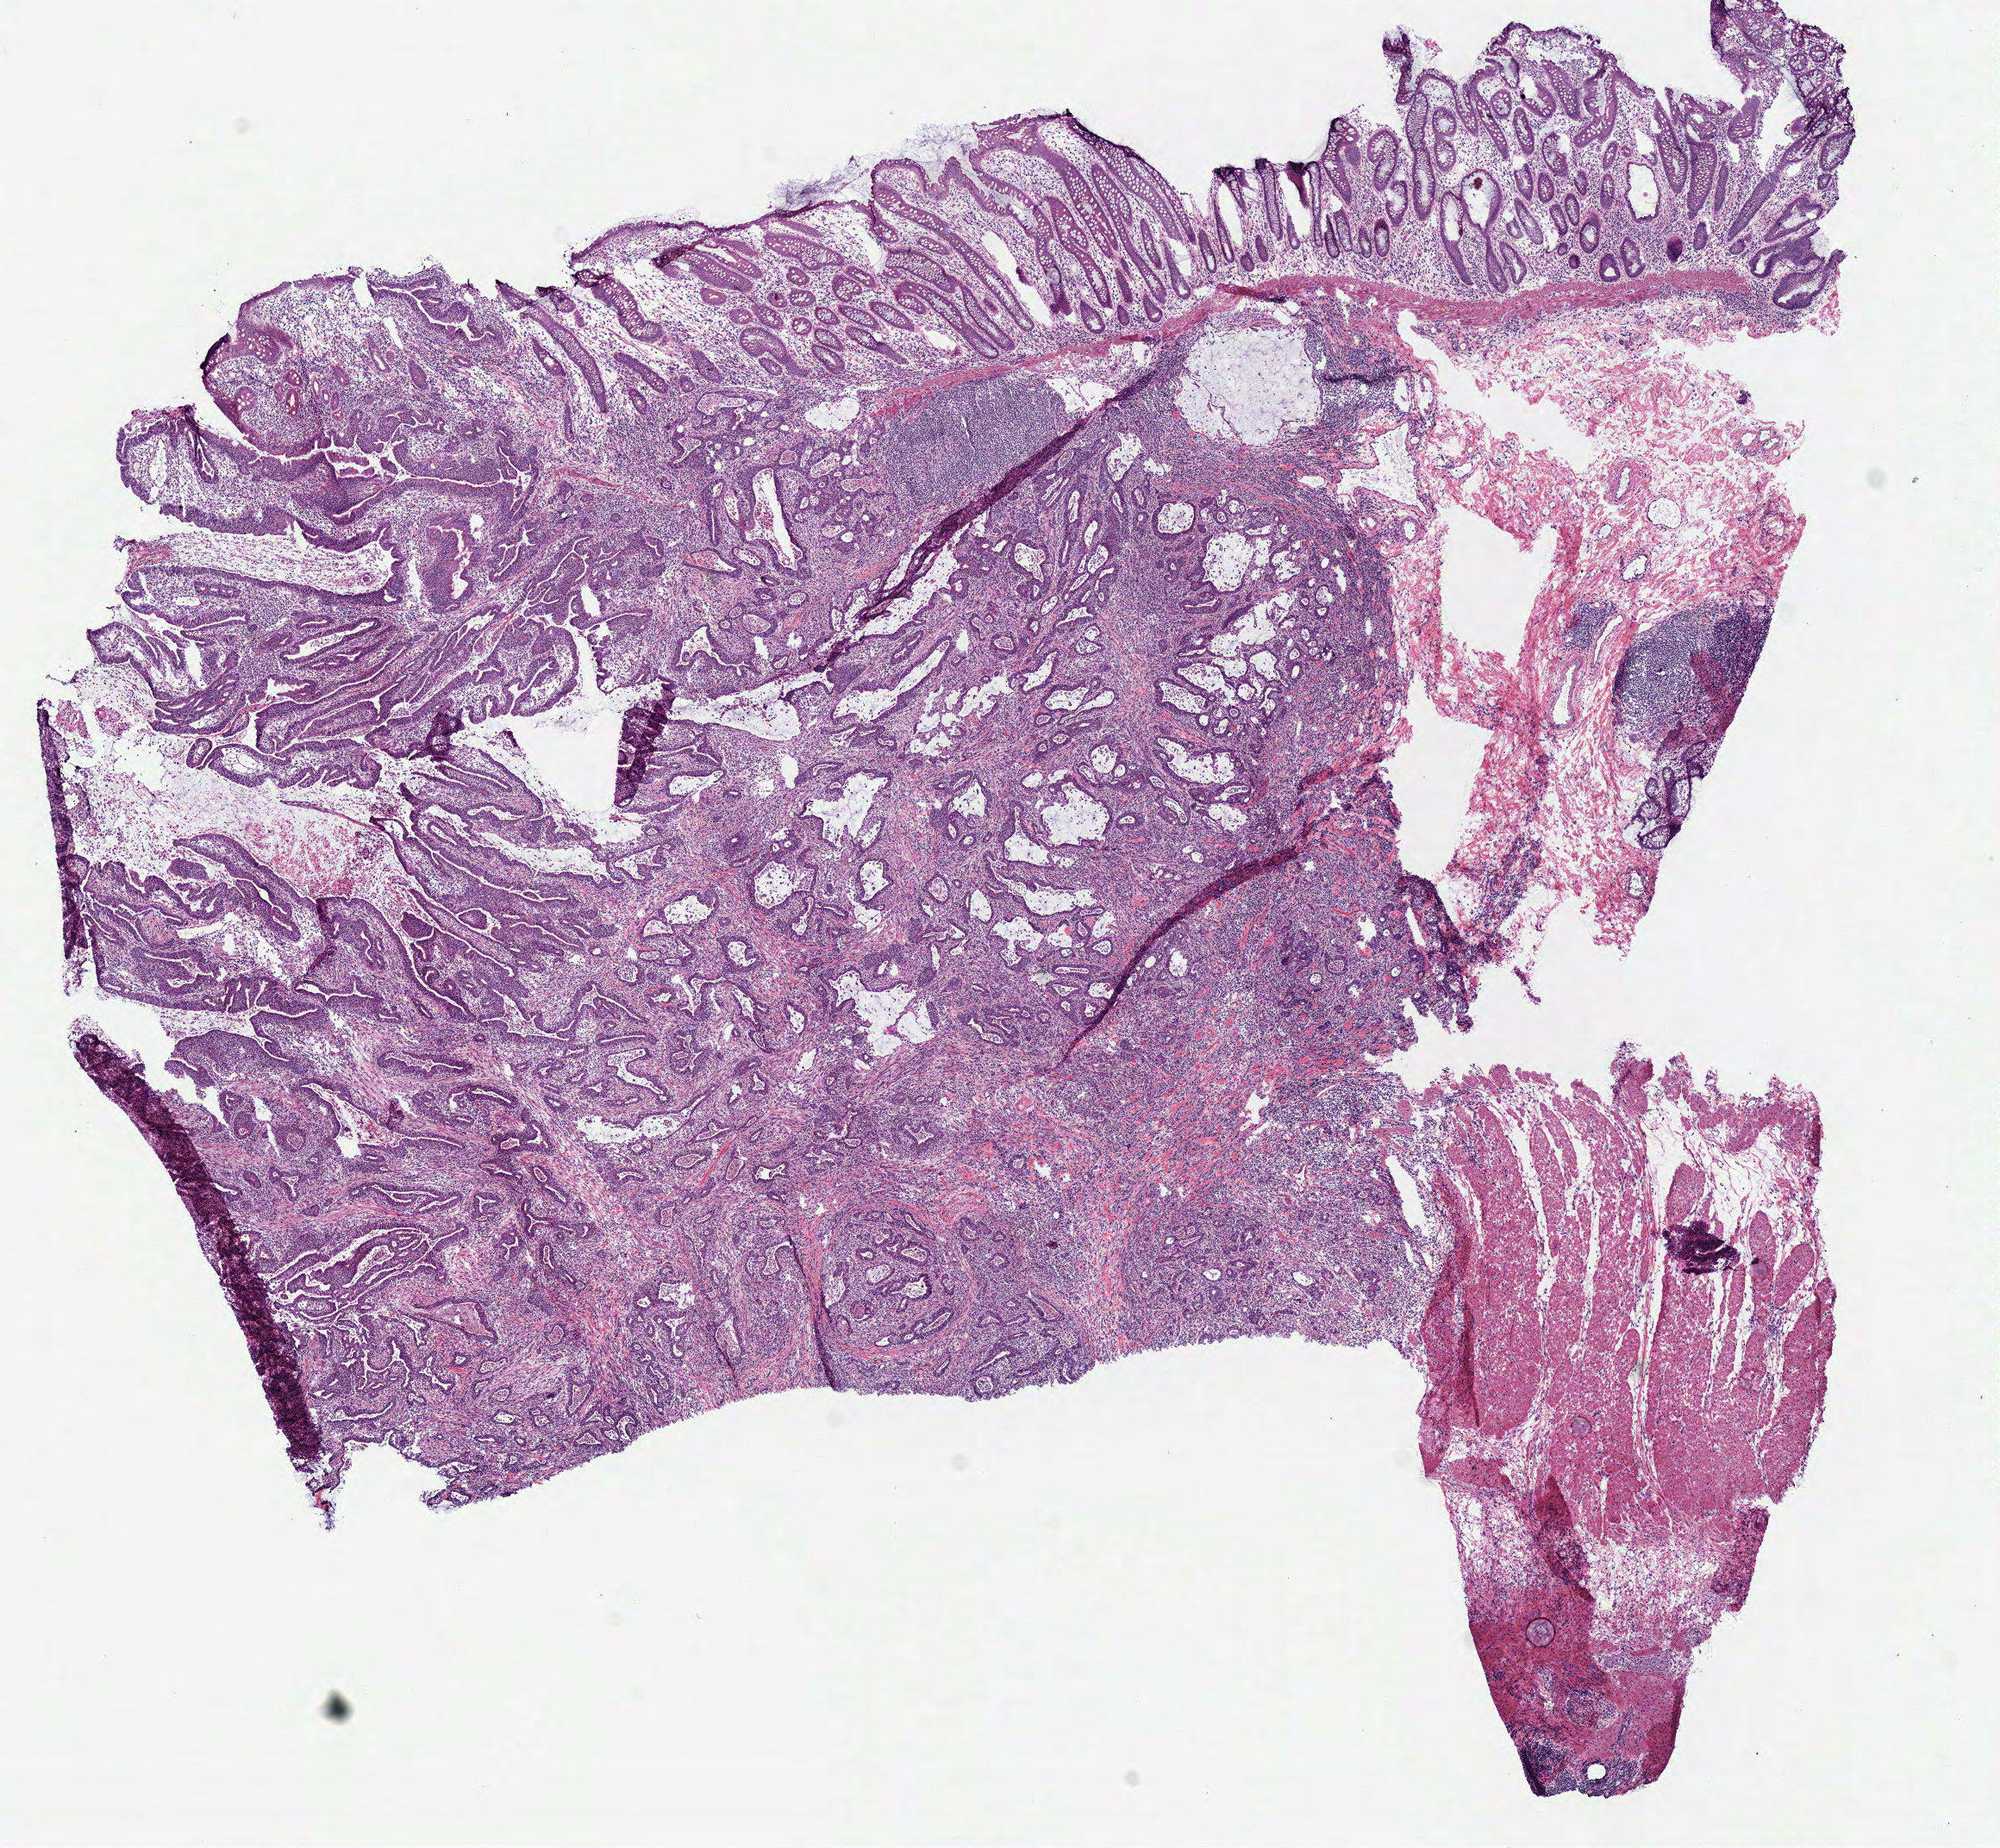
Digitized H&E-stained tissue section (whole slide), a low-resolution overview of the entire scanned area, about 9.1 x 8.4 mm (acquisition: 40x scan). Frozen section from the bottom of the tissue portion. Colon, primary tumour sample. Male, age 80 years at initial diagnosis. Composition of this section per pathologist review: tumour cells 35%, tumour nuclei 40%, normal cells 22%, stromal cells 40%, necrosis 3%. Infiltration values recorded for this section: lymphocyte infiltration 40%, monocyte infiltration 0%, neutrophil infiltration 5%.
• AJCC pathologic stage: IIA (7th edition)
• lymph nodes positive (case pathology): 0 of 18 examined
• diagnosis: Mucinous adenocarcinoma (hepatic flexure of colon)